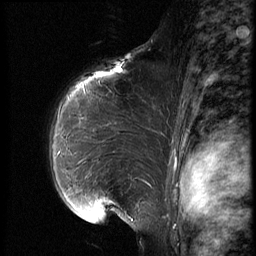
Breast MRI (dynamic contrast-enhanced), one sagittal slice; position 48 of 66 along the scan axis; dynamic contrast-enhanced series, image 2 of 3 at this slice position (ordered by acquisition); 1.5 T; TE 4.2 ms, TR 8.9 ms; 2.5 mm slice thickness; 256 × 256 image matrix, field of view 200 × 200 mm. Female patient, age 39 years. From the clinical record (not read from this slice): setting: breast cancer imaged before/during neoadjuvant chemotherapy; receptor status: HER2-positive.
Annotated regions visible in this slice (semi-automatic segmentation, software-assisted and operator-edited):
- analysis volume of interest (the breast-tissue region the enhancement analysis was run in; not a lesion): bounding box (x1, y1, x2, y2) in pixels: (45, 75, 170, 218)
- tumour enhancement mask (voxels above the 140 % enhancement threshold inside the analysis volume of interest): (89, 173, 94, 175)